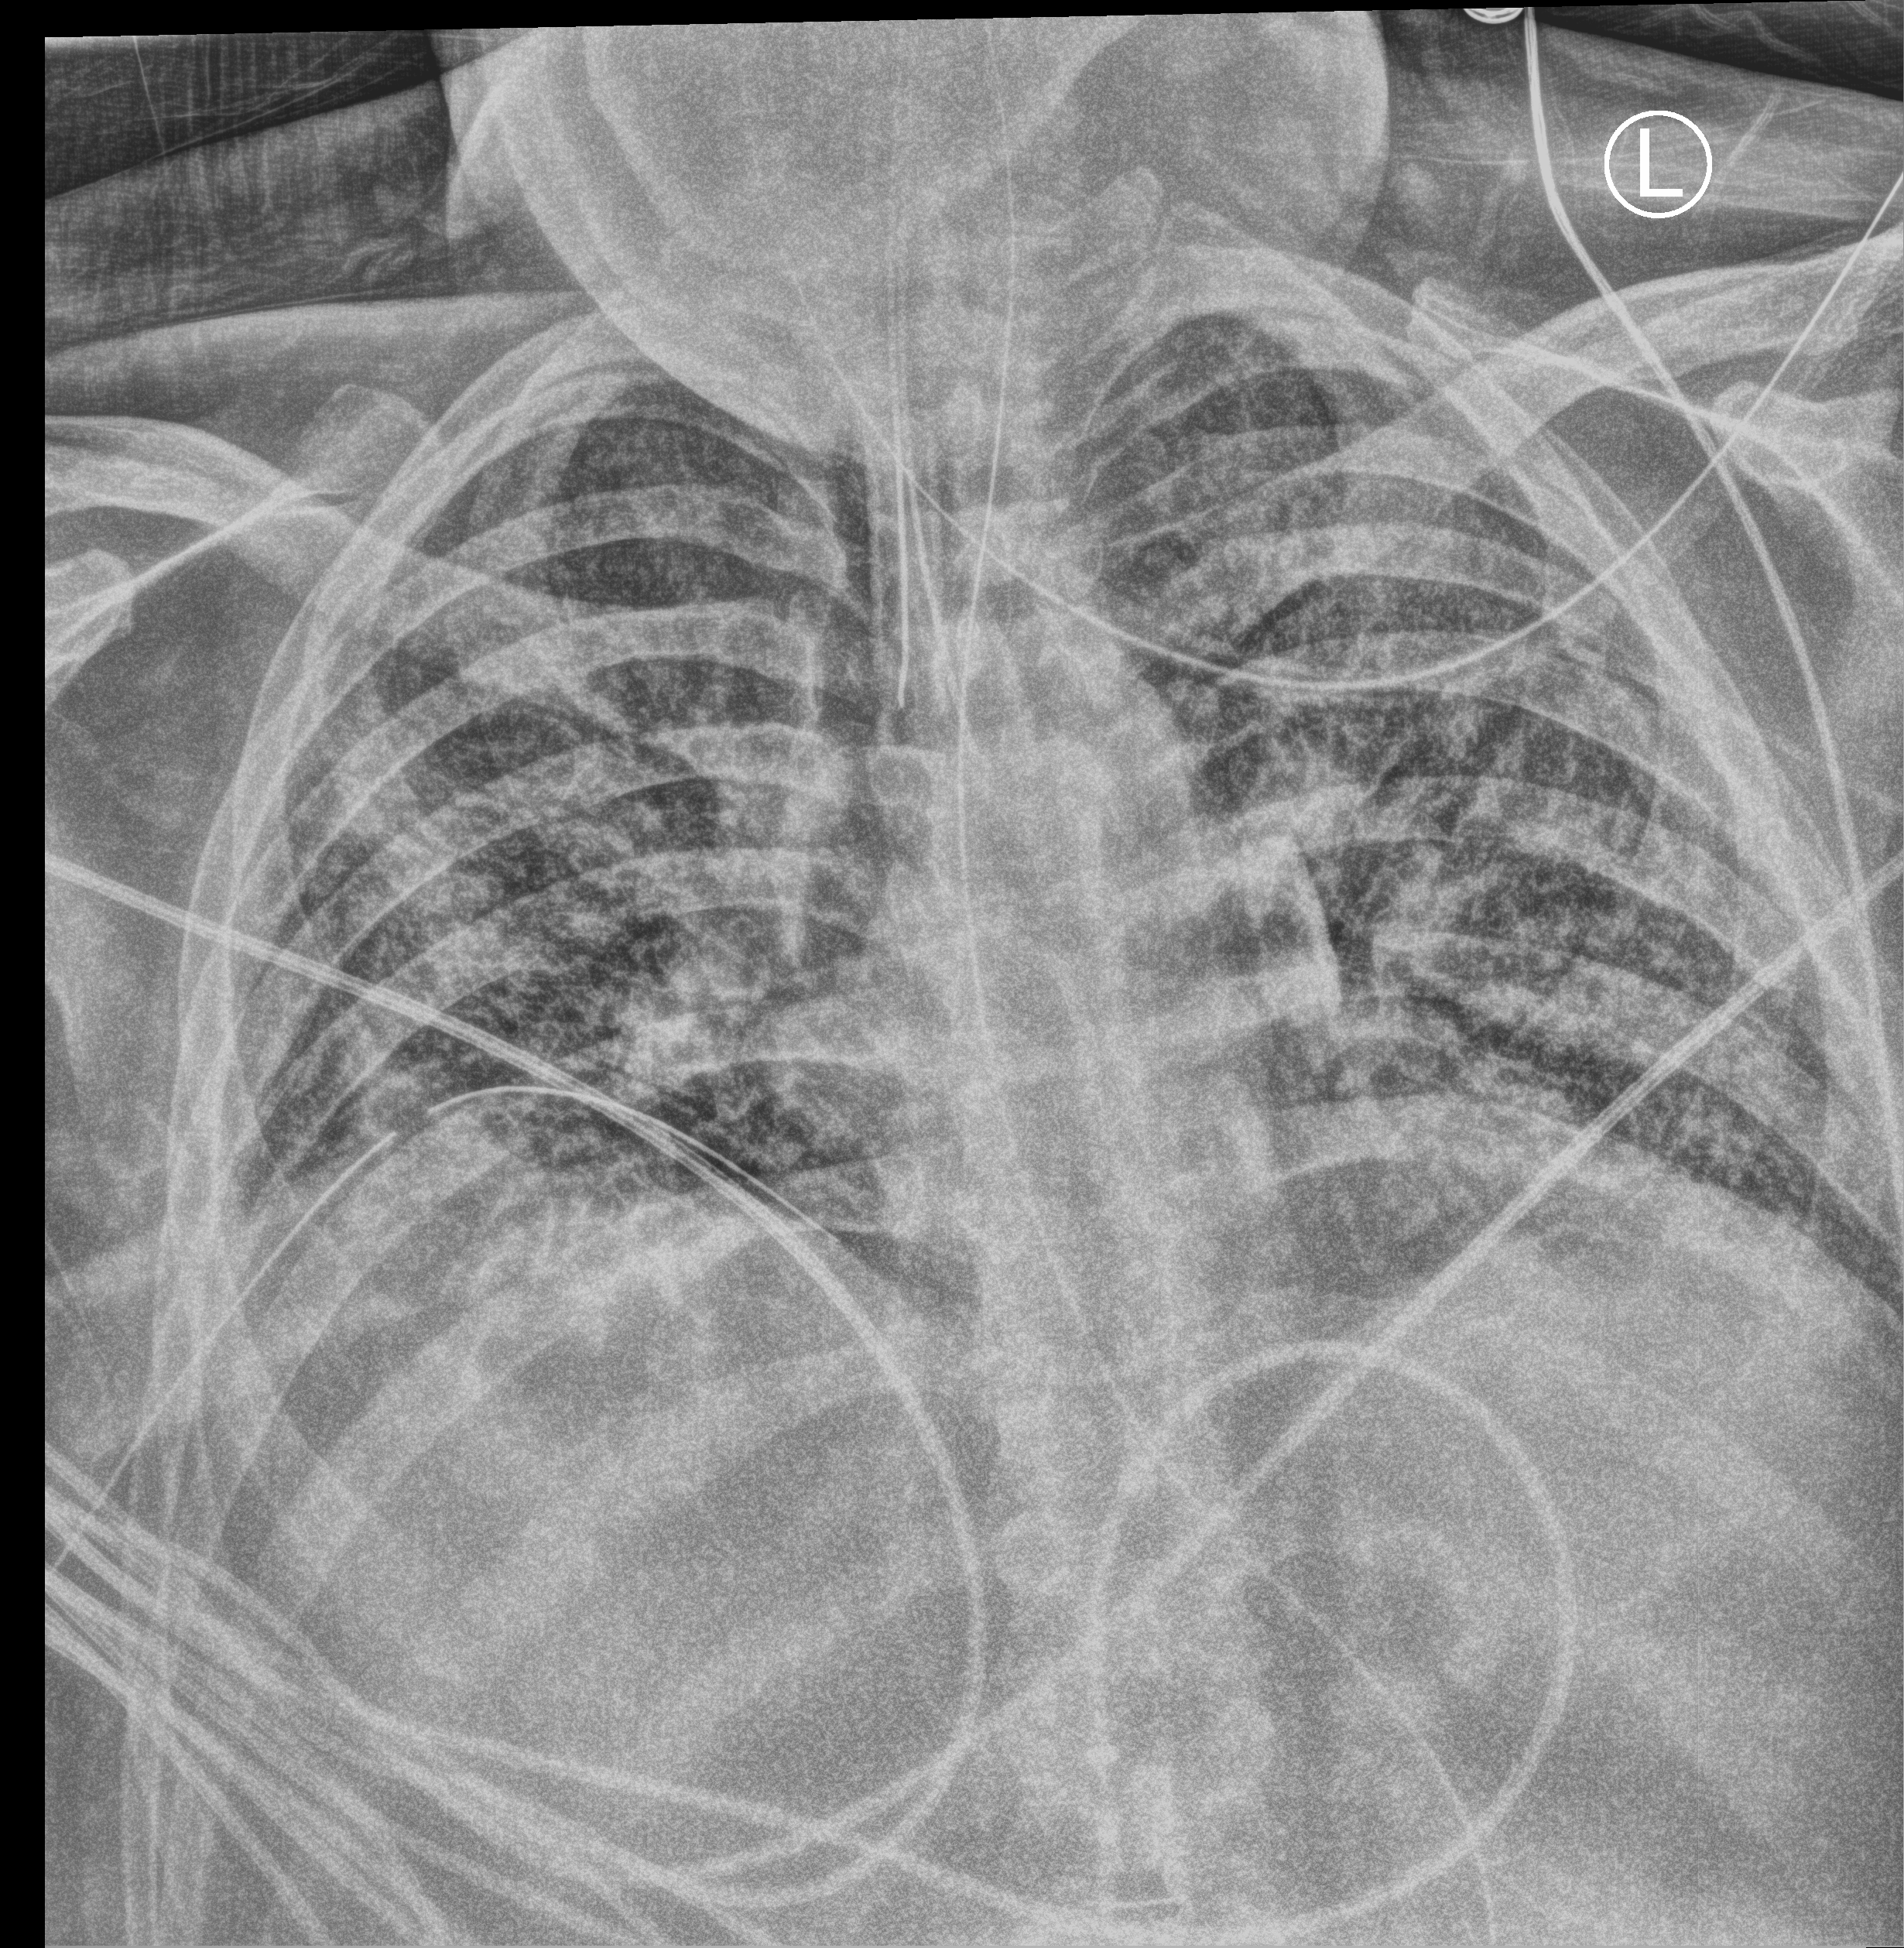
Chest X-ray (portable), anteroposterior (AP) projection. Male patient hospitalised with COVID-19, age 18–59 years.
From the hospital-stay record, not from the radiograph (when in the stay this image was taken is not recorded): other chronic lung disease (admission record): no; admitted to intensive care during this hospital stay: yes; mechanically ventilated during this hospital stay: yes.